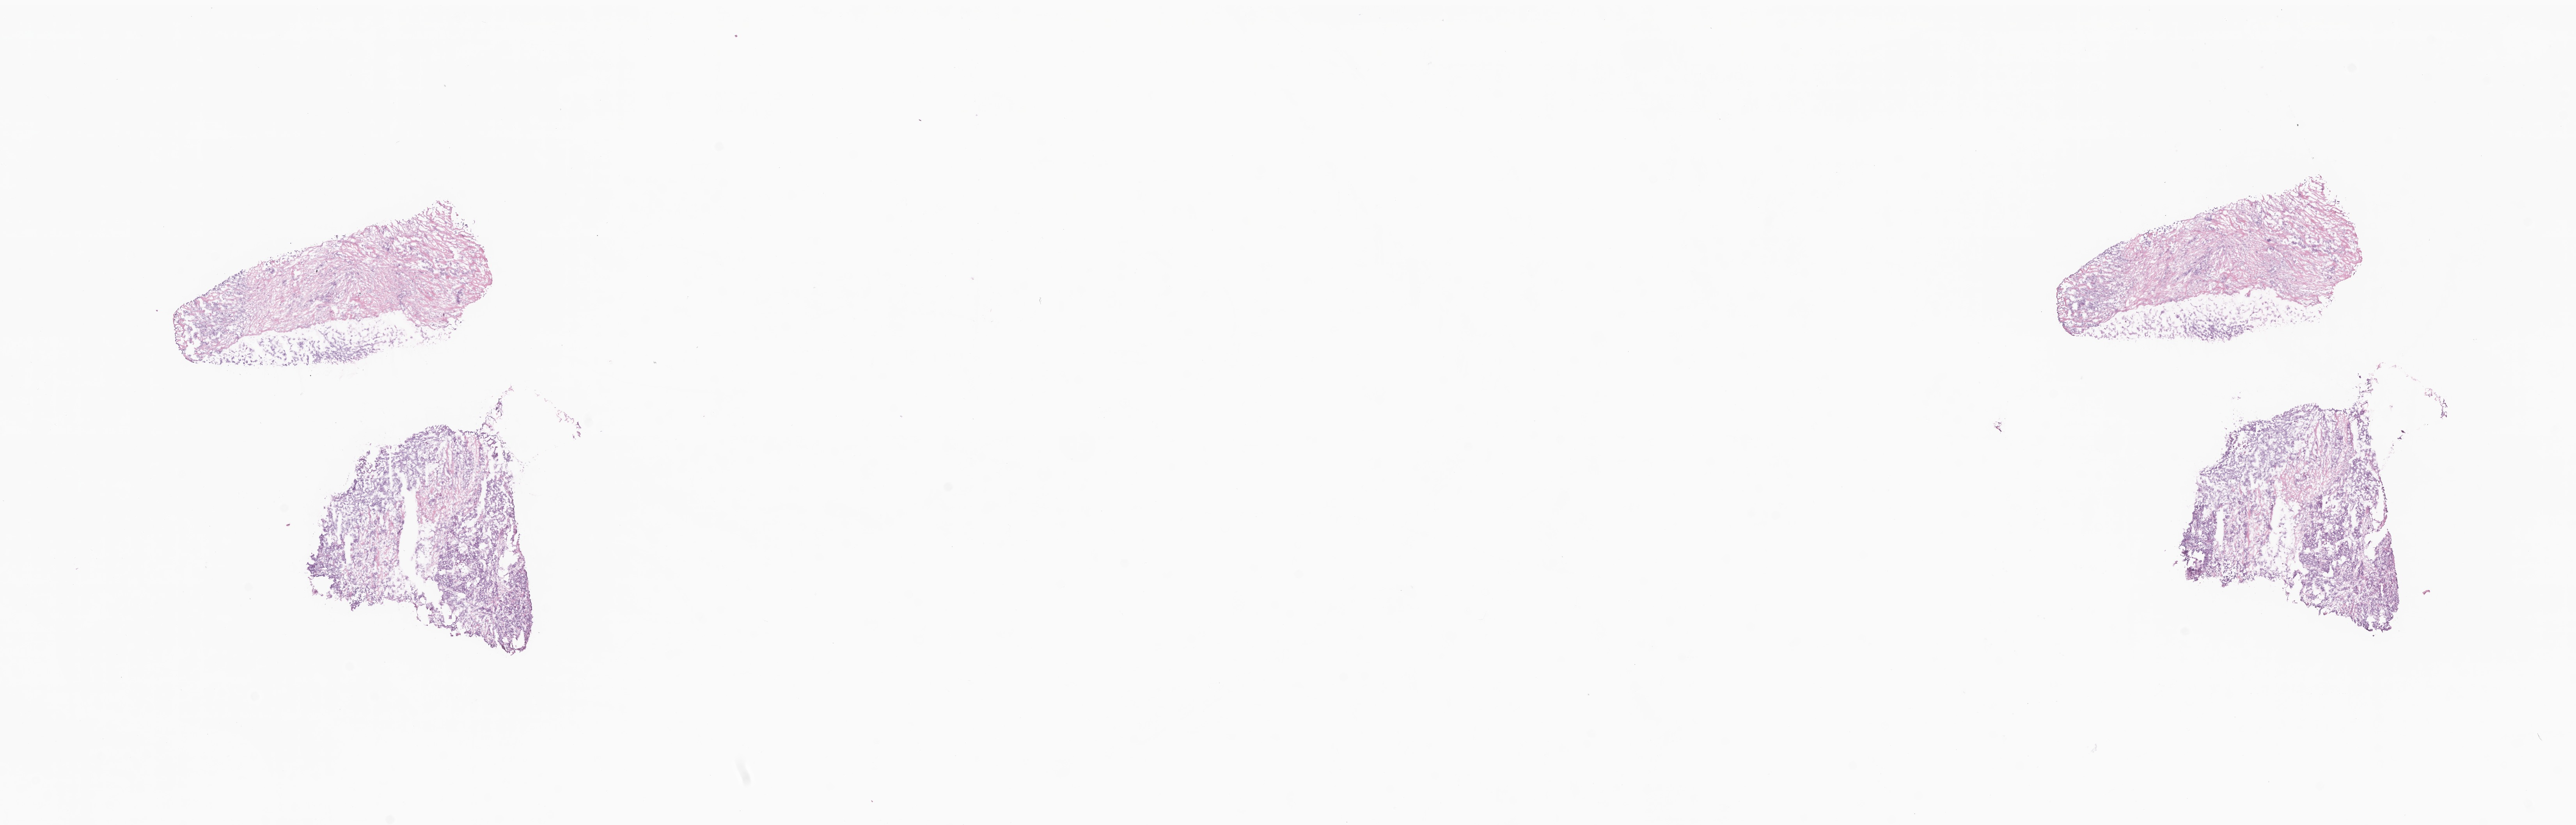
Haematoxylin and eosin whole-slide image — whole scanned area (about 27.8 x 8.9 mm) shown as a low-resolution overview; cryosection; specimen: primary tumor; anatomic site: breast (left). Female patient; age at initial diagnosis 73 years. Pathologist review of this section (percent, as recorded): tumor cells 60%, tumor nuclei 77%, stromal cells 21%, necrosis 1%, normal cells 18%. Inflammatory infiltration, as recorded: lymphocyte infiltration 0%, monocyte infiltration 0%, neutrophil infiltration 0%.
Section: top of the tissue portion. Histologic diagnosis: Infiltrating duct carcinoma, NOS.